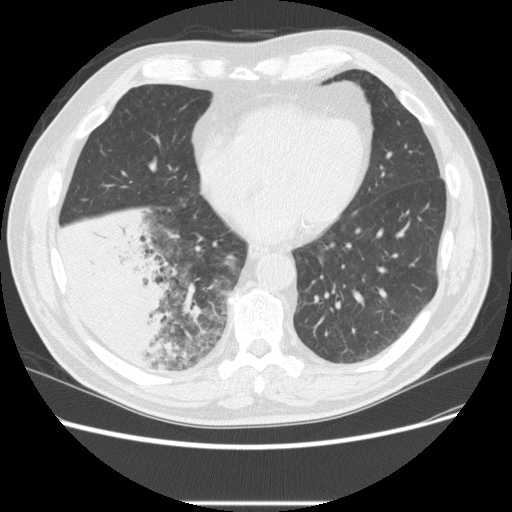
Low-dose screening chest CT, one axial slice. Position 82 of 233 along the scan axis. Reconstruction kernel STANDARD. 120 kVp. Lung window (W 1500 / L -600 HU). 512 × 512 image matrix, field of view 380 × 380 mm.
Outlined on this slice (outlined manually by an expert reader):
- lesion 3 (tumor, lower lobe of right lung): box from (x=56, y=208) to (x=176, y=365) px